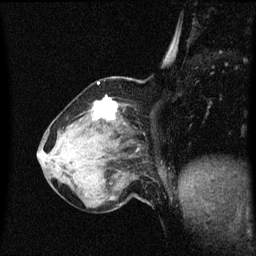
Breast MRI (dynamic contrast-enhanced), one sagittal slice. Slice 19 of 60 in the series (ordered by position). Dynamic contrast-enhanced series, image 2 of 3 at this slice position (ordered by acquisition). 1.5 T. TE 4.2 ms, TR 8.4 ms. 256 × 256 image matrix, field of view 200 × 200 mm. Patient: female, 64 years. Case-level facts recorded for this patient, not image findings: setting: breast cancer imaged before/during neoadjuvant chemotherapy; receptor status: HR-positive, HER2-negative.
Annotated regions visible in this slice (semi-automatic segmentation, software-assisted and operator-edited):
- analysis volume of interest (the breast-tissue region the enhancement analysis was run in; not a lesion): bounding box <58,98,137,167> (left, top, right, bottom; pixels)
- tumour enhancement mask (voxels above the 70 % enhancement threshold inside the analysis volume of interest): <96,98,117,121>